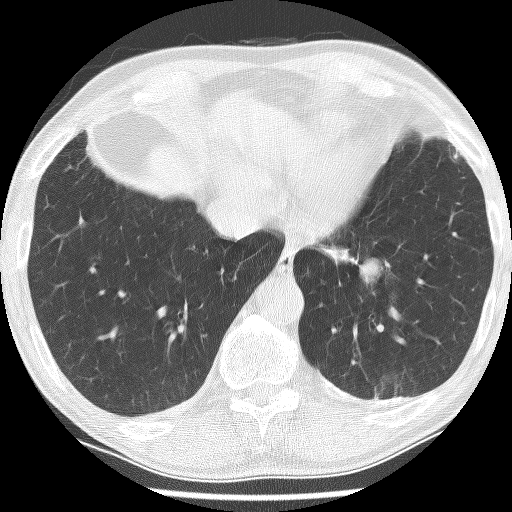
Low-dose screening chest CT, axial slice; first (baseline) screen; lung window (W 1500 / L -600 HU); 2.5 mm slice thickness; slice 188 of 226 in the series. Male participant, aged 74 years at enrolment. Current smoker at enrolment.
Expert reader's lesion annotation, box from (x=311, y=212) to (x=409, y=304) px. Screening reader's record for this exam (one nodule recorded; not confirmed to be the boxed lesion): non-calcified nodule or mass ≥4 mm, left lower lobe, 30 × 27 mm, spiculated (stellate) margins, soft tissue attenuation. Official screen result: positive, change unspecified: nodule(s) >= 4 mm or enlarging nodule(s), mass(es), or other non-specific abnormalities suspicious for lung cancer. Lung cancer was diagnosed 151 days after this screen: adenocarcinoma, NOS, left lower lobe, stage IIIA (AJCC 6th edition), 49 mm at pathology.